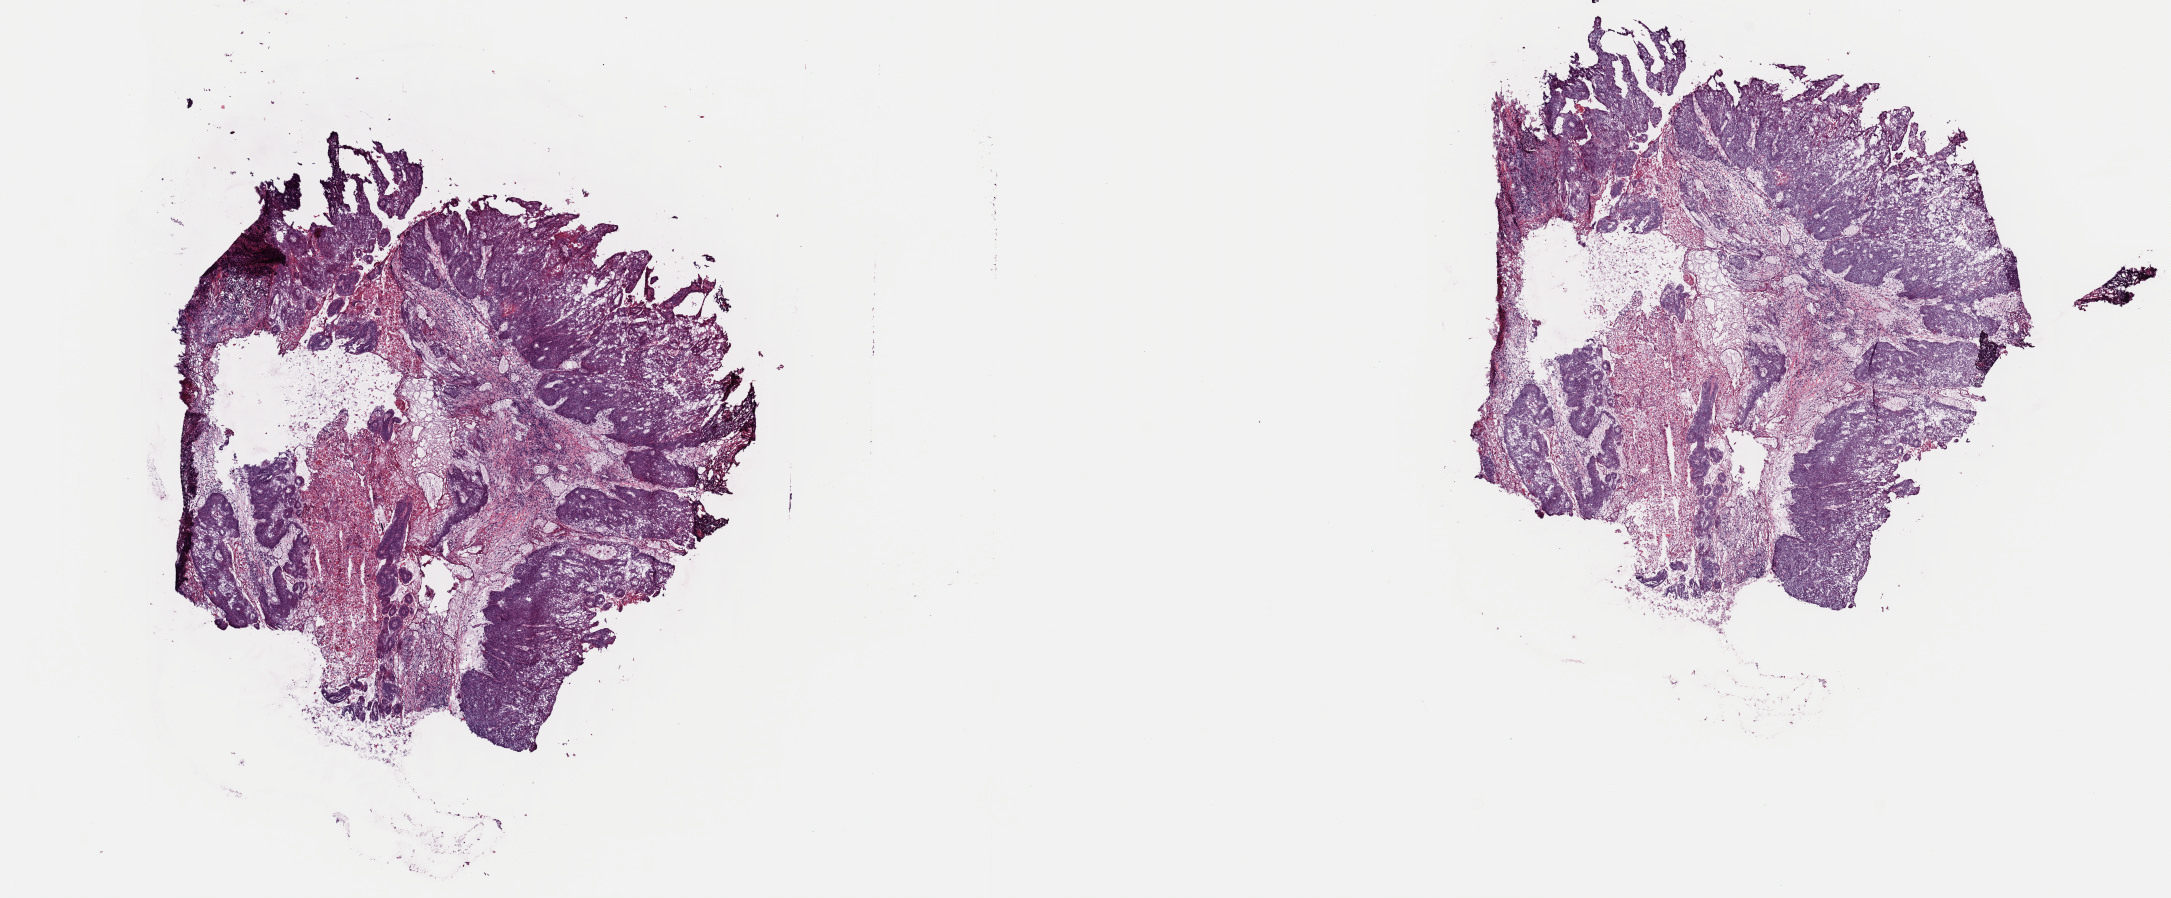
Digitized H&E tissue section (whole slide), shown as a low-resolution overview of the whole scanned area (about 17.2 x 7.1 mm), frozen section from the top of the tissue portion, primary tumour sample from the head and neck. Patient: male, age at initial diagnosis 44 years. Histologic grade: G2 (moderately differentiated). Composition of this section per pathologist review: tumour cells 80%, tumour nuclei 75%, normal cells 20%, stromal cells 0%, necrosis 0%. Infiltration values recorded for this section: lymphocyte infiltration 10%, monocyte infiltration 0%, neutrophil infiltration 0%.
Histologic diagnosis: Squamous cell carcinoma, keratinizing, NOS (floor of mouth, NOS). AJCC pathologic stage: IVA (7th edition).